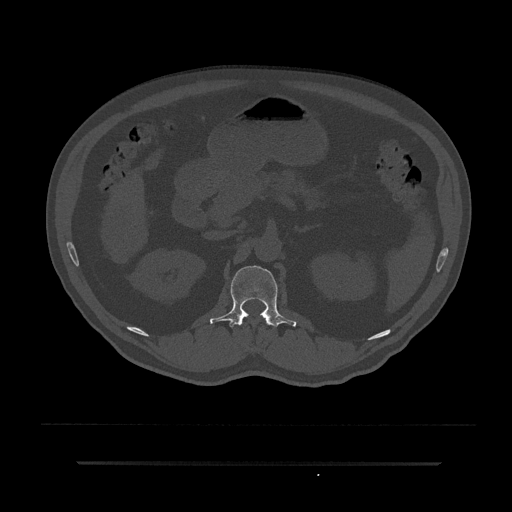
CT including the spine, one axial slice; slice 155 of 797 in the series (ordered by position); 120 kVp; bone window (W 1800 / L 400 HU); 0.5 mm slice thickness; 512 × 512 image matrix, field of view 464 × 464 mm. Patient: male, 59 years. Case-level facts recorded for this patient, not image findings: primary cancer: bile ducts; vertebrae with lytic lesions (as recorded): T10.
Structures marked on this image (semi-automatically segmented with operator editing):
- L1 vertebra: bounding box <210,265,296,327> (left, top, right, bottom; pixels)